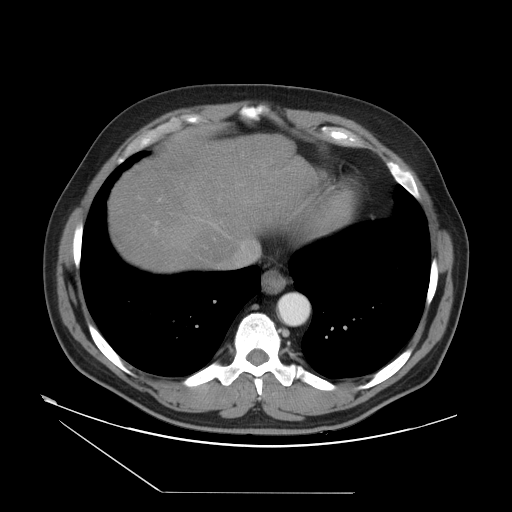
Contrast-enhanced abdominal CT, one axial slice. Slice 46 of 55 in the series (ordered by position). Reconstruction kernel STANDARD. 120 kVp. Soft-tissue window (W 400 / L 40 HU). 5 mm slice thickness. 512 × 512 image matrix, field of view 454 × 454 mm. Male patient, age 59 years. Case-level facts recorded for this patient, not image findings: diagnosis: colorectal cancer liver metastases, imaged before liver resection; multiple liver metastases: yes; largest metastasis: 0.3 cm; disease in both lobes: yes.
Outlined on this slice (expert manual segmentation):
- hepatic veins: box from (x=218, y=243) to (x=244, y=267) px
- liver: (x=112, y=141)–(x=313, y=268)
- planned liver remnant (the part of the liver to remain after resection): (x=112, y=171)–(x=233, y=268)
- portal vein (with intrahepatic branches): (x=155, y=200)–(x=160, y=233)
- liver metastasis: (x=252, y=186)–(x=255, y=191)